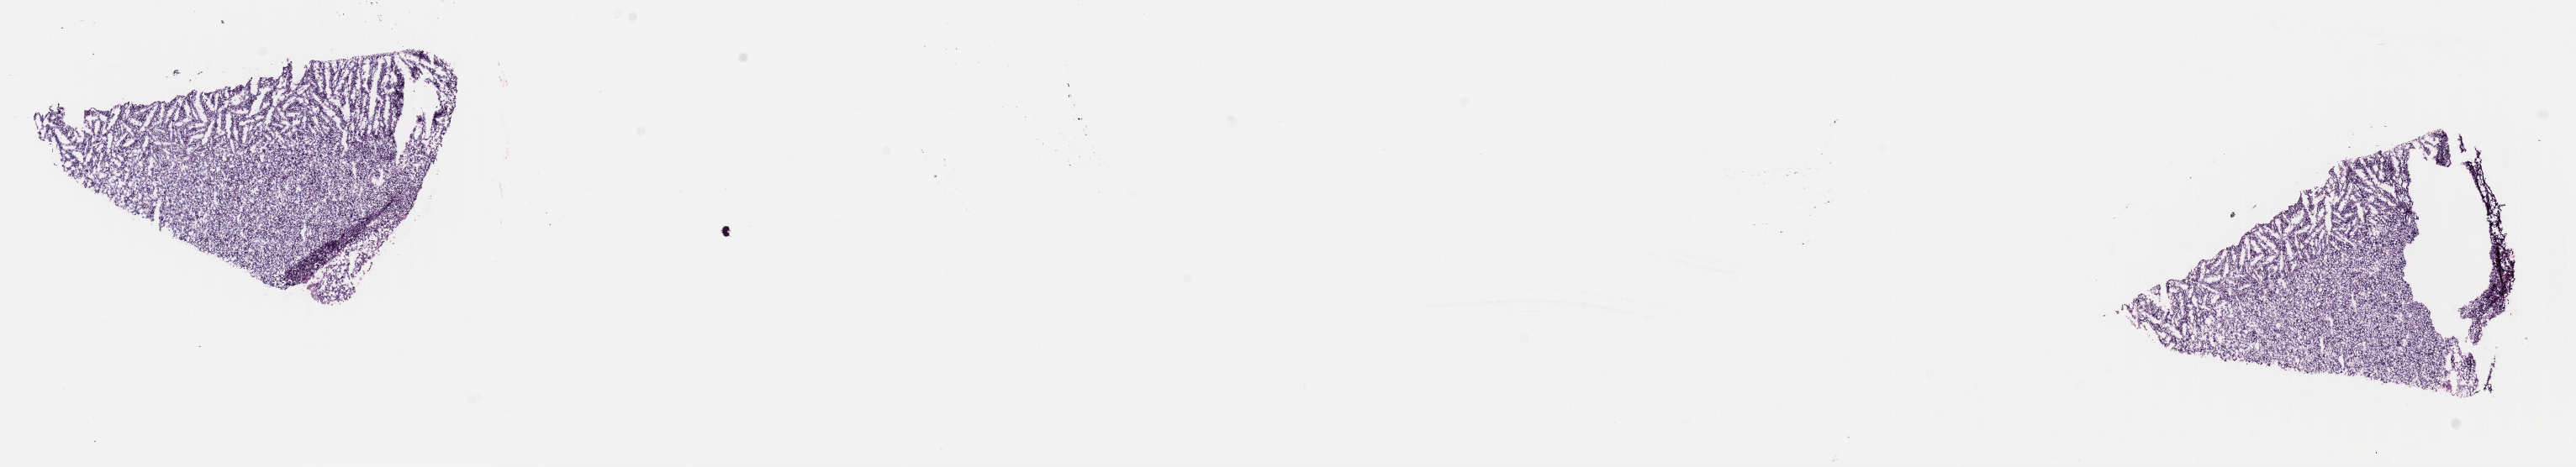
Digitized Hematoxylin and eosin (H&E) stained tissue section (whole slide) — whole scanned area (about 24.2 x 4.4 mm) shown as a low-resolution overview; frozen section; primary tumour sample from the retroperitoneum and peritoneum. Male patient; age at initial diagnosis 60 years. Pathologist review of this section (percent, as recorded): tumour cells 95%, tumour nuclei 95%, normal cells 0%, stromal cells 5%, necrosis 0%. Inflammatory infiltration, as recorded: lymphocyte infiltration 0%, monocyte infiltration 0%, neutrophil infiltration 0%.
- diagnosis: Dedifferentiated liposarcoma (retroperitoneum)